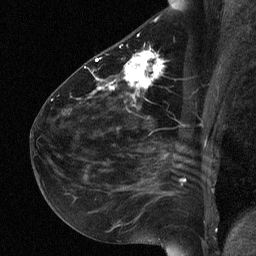
Breast MRI (dynamic contrast-enhanced), one sagittal slice; position 34 of 64 along the scan axis; dynamic contrast-enhanced study with each time point stored as its own series, time point 2 of 3 at this slice position (early post-contrast, ordered by acquisition time); 1.5 T; TE 4.8 ms, TR 27 ms; 256 × 256 image matrix, field of view 180 × 180 mm. Patient: female, 51 years. Case-level facts recorded for this patient, not image findings: setting: breast cancer imaged before/during neoadjuvant chemotherapy; receptor status: HR-positive, HER2-negative.
Annotated regions visible in this slice (semi-automatically segmented with operator editing):
- analysis volume of interest (the breast-tissue region the enhancement analysis was run in; not a lesion): bounding box [x1, y1, x2, y2] px = [72, 34, 165, 118]
- tumour enhancement mask (voxels above the 90 % enhancement threshold inside the analysis volume of interest): [96, 51, 162, 97]